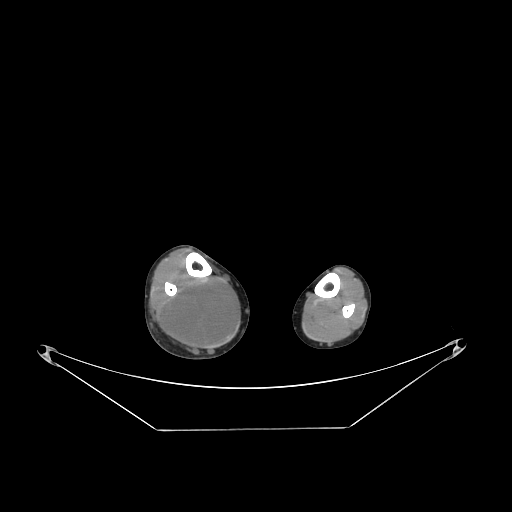
CT of an extremity soft-tissue mass (from a PET/CT study), one axial slice. 140 kVp. Soft-tissue window (W 400 / L 40 HU). 512 × 512 image matrix. Male patient. From the clinical record (not read from this slice): histological type: liposarcoma - round cell; grade: high; site of the primary tumour: right calf.
Annotated regions visible in this slice (expert contour drawn on MRI and transferred to this co-registered scan by the dataset authors):
- gross tumour volume (mass): bounding box (x1, y1, x2, y2) in pixels: (164, 279, 239, 348)